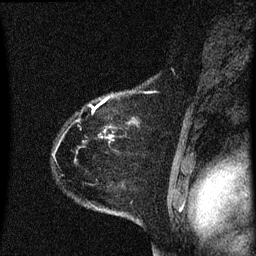
Breast MRI (dynamic contrast-enhanced), one sagittal slice. Position 52 of 60 along the scan axis. Dynamic contrast-enhanced series, image 2 of 3 at this slice position (ordered by acquisition). 1.5 T. TE 4.2 ms, TR 8.4 ms. 256 × 256 image matrix, field of view 200 × 200 mm. Patient: female, 35 years. From the clinical record (not read from this slice): setting: breast cancer imaged before/during neoadjuvant chemotherapy; receptor status: HER2-positive.
Outlined on this slice (semi-automatic segmentation, software-assisted and operator-edited):
- analysis volume of interest (the breast-tissue region the enhancement analysis was run in; not a lesion): box from (x=55, y=74) to (x=174, y=173) px
- tumour enhancement mask (voxels above the 70 % enhancement threshold inside the analysis volume of interest): (x=92, y=96)–(x=112, y=137)